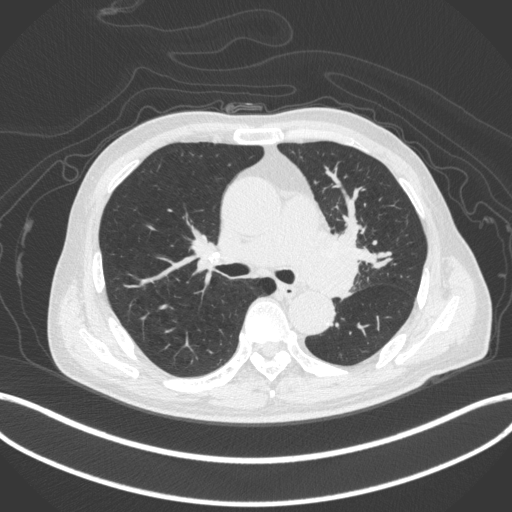
Chest CT, one axial slice; slice 267 of 420 in the series (ordered by position); reconstruction kernel B31f; 120 kVp; lung window (W 1500 / L -600 HU); 1 mm slice thickness; 512 × 512 image matrix, field of view 400 × 400 mm. Male patient, age 77 years. From the clinical record (not read from this slice): clinical TNM (as recorded): T3 N1 M0.
Annotated regions visible in this slice (bounding box drawn by a radiologist):
- lung tumour (recorded histology: adenocarcinoma): bounding box <298,225,363,295> (left, top, right, bottom; pixels)